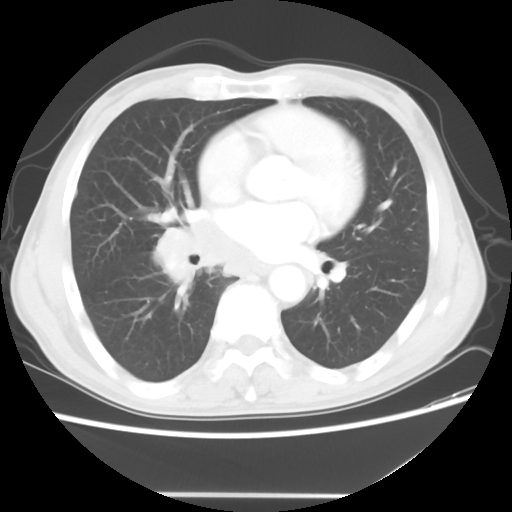
Chest CT, one axial slice; slice 24 of 56 in the series (ordered by position); reconstruction kernel STANDARD; 120 kVp; lung window (W 1500 / L -600 HU); 512 × 512 image matrix, field of view 344 × 344 mm. Patient: male, 65 years. From the clinical record (not read from this slice): clinical TNM (as recorded): T1c N3 M0; histopathological grade: G3.
Outlined on this slice (bounding box drawn by a radiologist):
- lung tumour (recorded histology: small cell carcinoma): bounding box <155,207,269,290> (left, top, right, bottom; pixels)